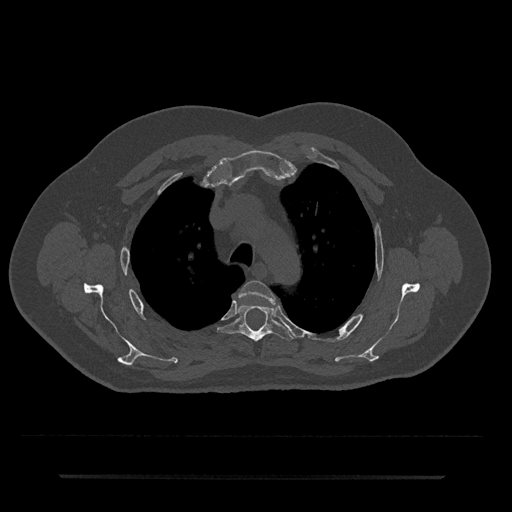
CT including the spine, one axial slice. Slice 538 of 797 in the series (ordered by position). Reconstruction kernel Br40s/3. Bone window (W 1800 / L 400 HU). 0.5 mm slice thickness. 512 × 512 image matrix, field of view 437 × 437 mm. Patient: male, 69 years. Case-level facts recorded for this patient, not image findings: primary cancer: prostate.
Annotated regions visible in this slice (semi-automatically segmented with operator editing):
- T3 vertebra: bounding box (x1, y1, x2, y2) in pixels: (239, 280, 275, 304)
- T4 vertebra: (219, 305, 293, 342)